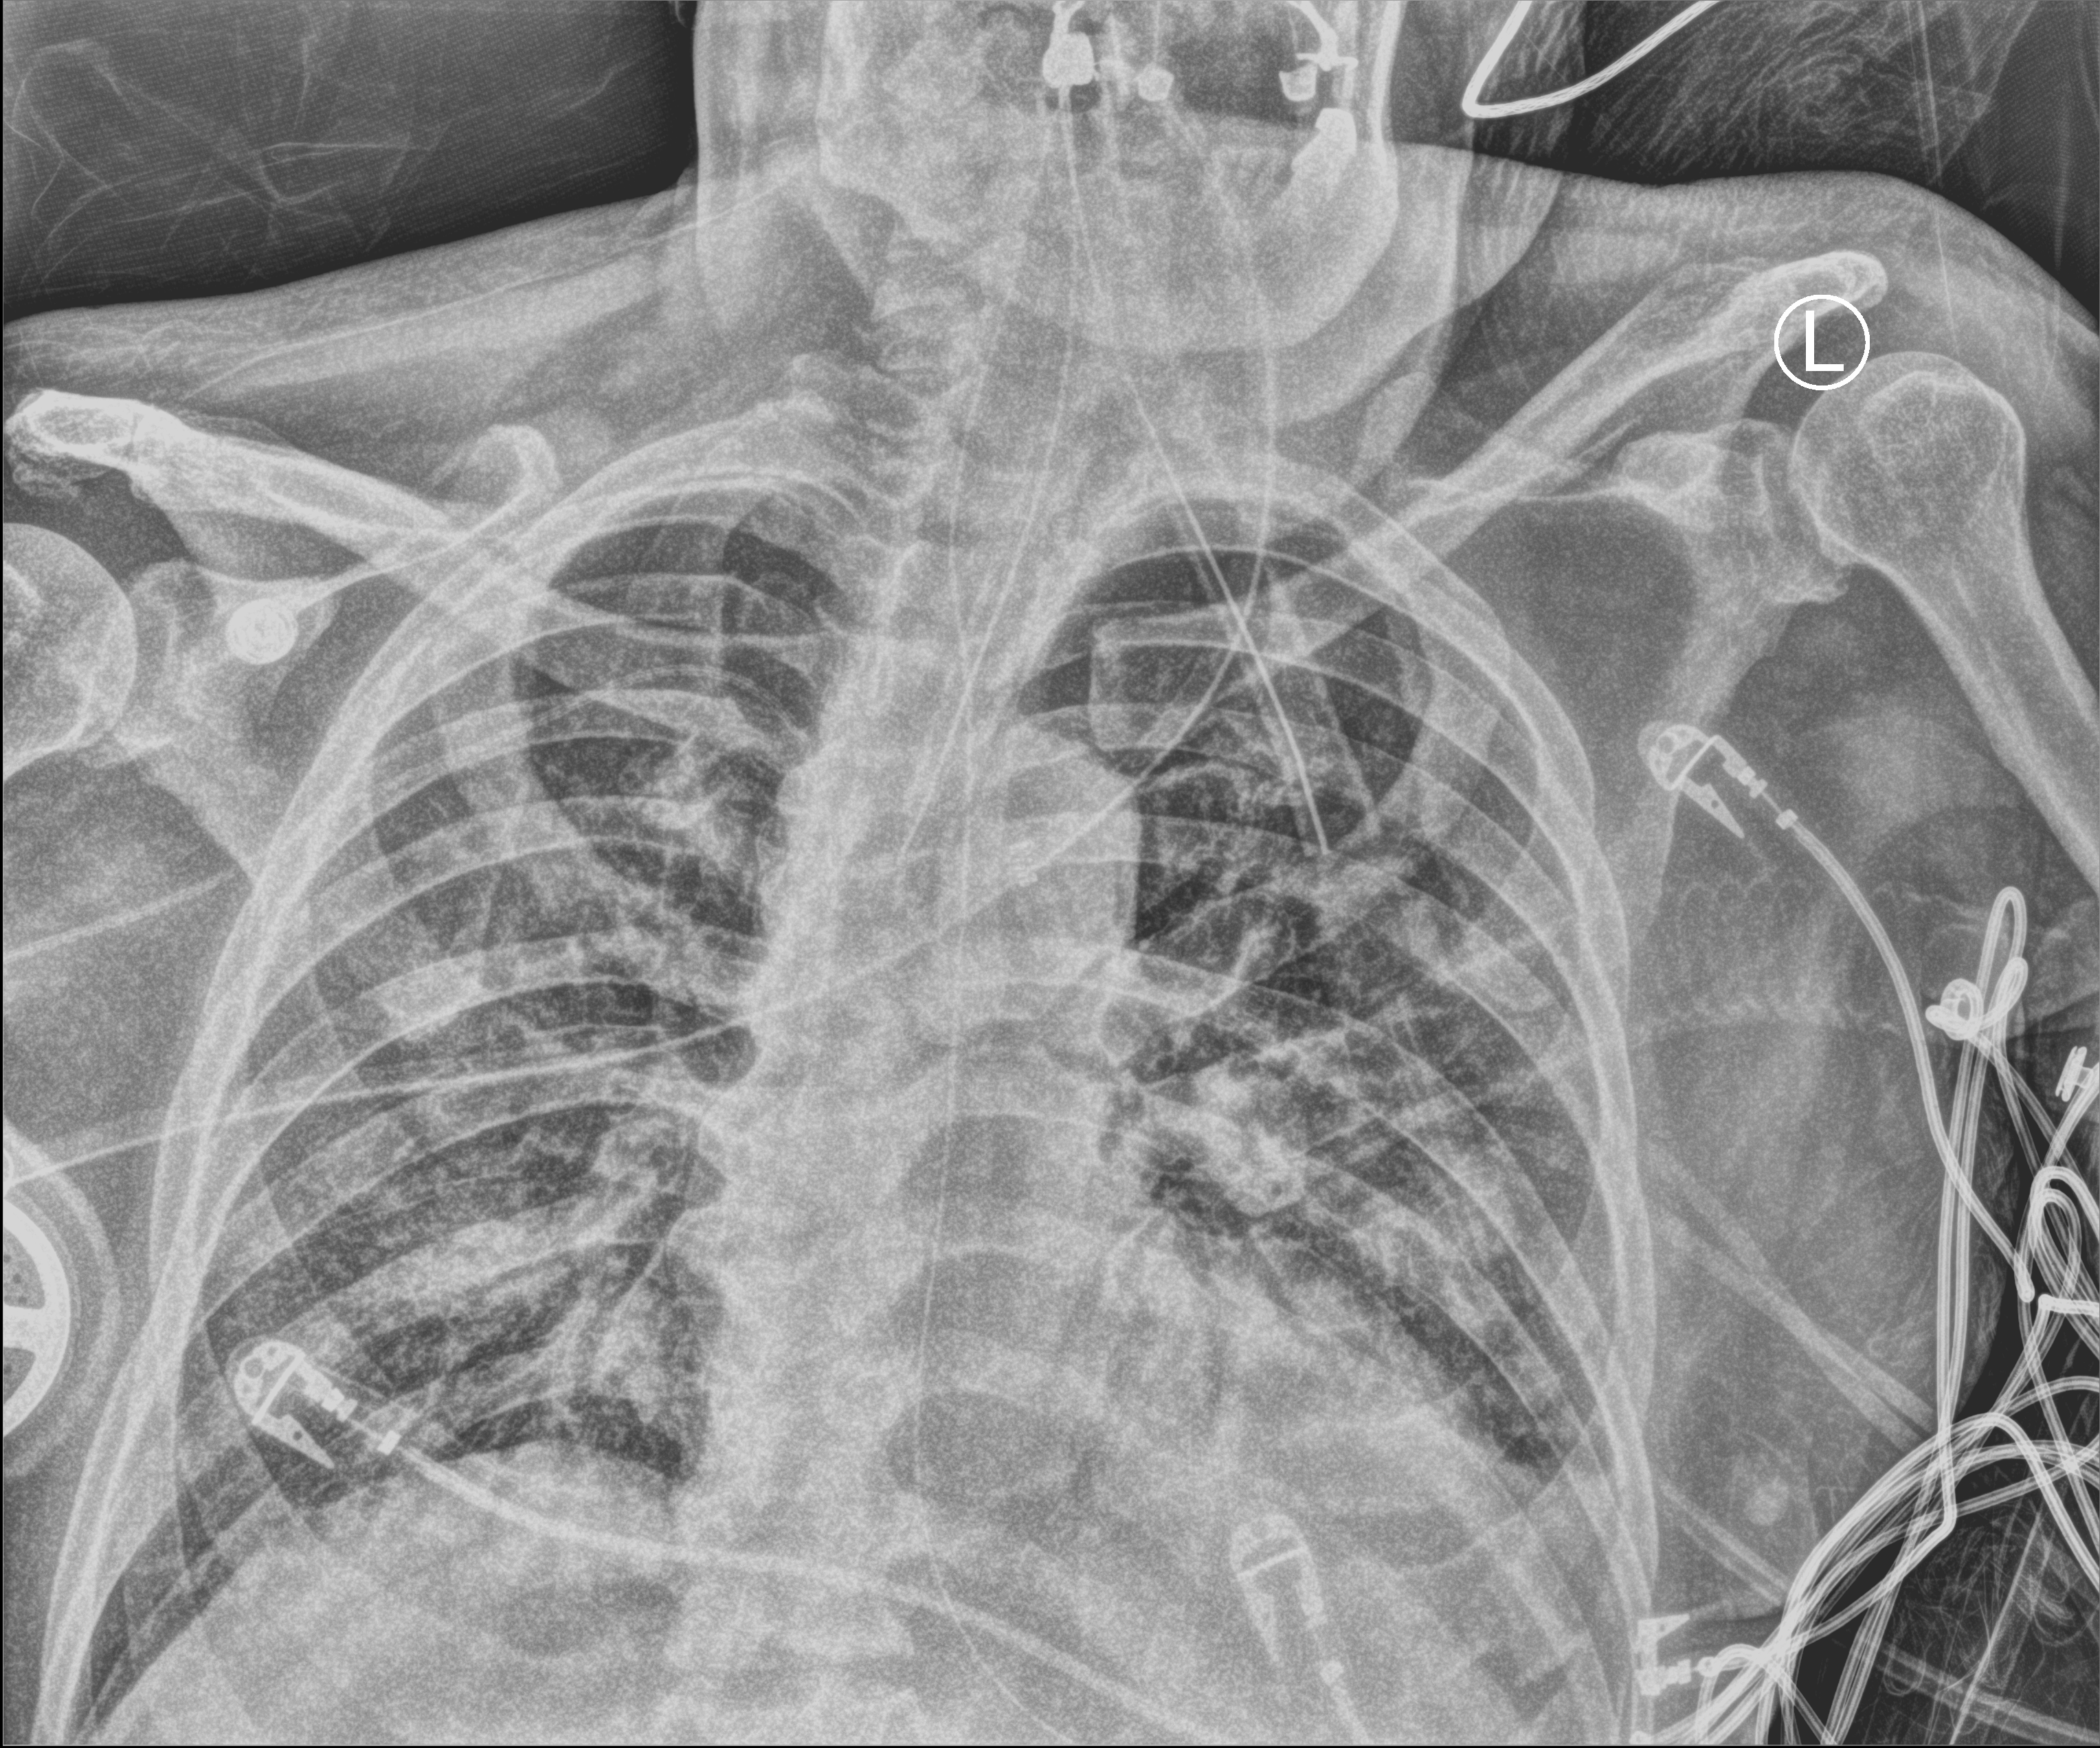
Portable chest radiograph. Patient hospitalised with COVID-19; male, aged 75–90 years.
Admission-level facts for this patient (not findings on this image; timing relative to this image not recorded):
- smoking status (admission record): former
- mechanically ventilated during this hospital stay: yes
- admitted to intensive care during this hospital stay: yes